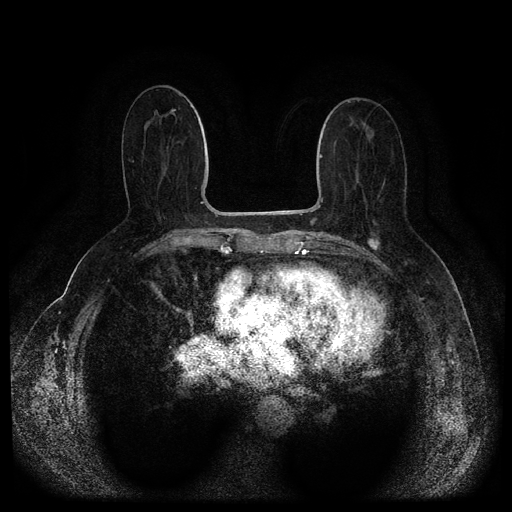
Breast MRI (dynamic contrast-enhanced, multi-phase), one axial slice. Position 45 of 116 along the scan axis. Dynamic contrast-enhanced series, time point 2 of 5 at this slice position (early post-contrast). 1.5 T. TE 2.6 ms, TR 5.4 ms. 2 mm slice thickness. 512 × 512 image matrix. Patient: female, 67 years.
Outlined on this slice (semi-automatically segmented with operator editing):
- breast lesion (labelled 'tumour' in the annotation; benign lesions carry a separate 'benign' label): bounding box [x1, y1, x2, y2] px = [366, 236, 382, 251]